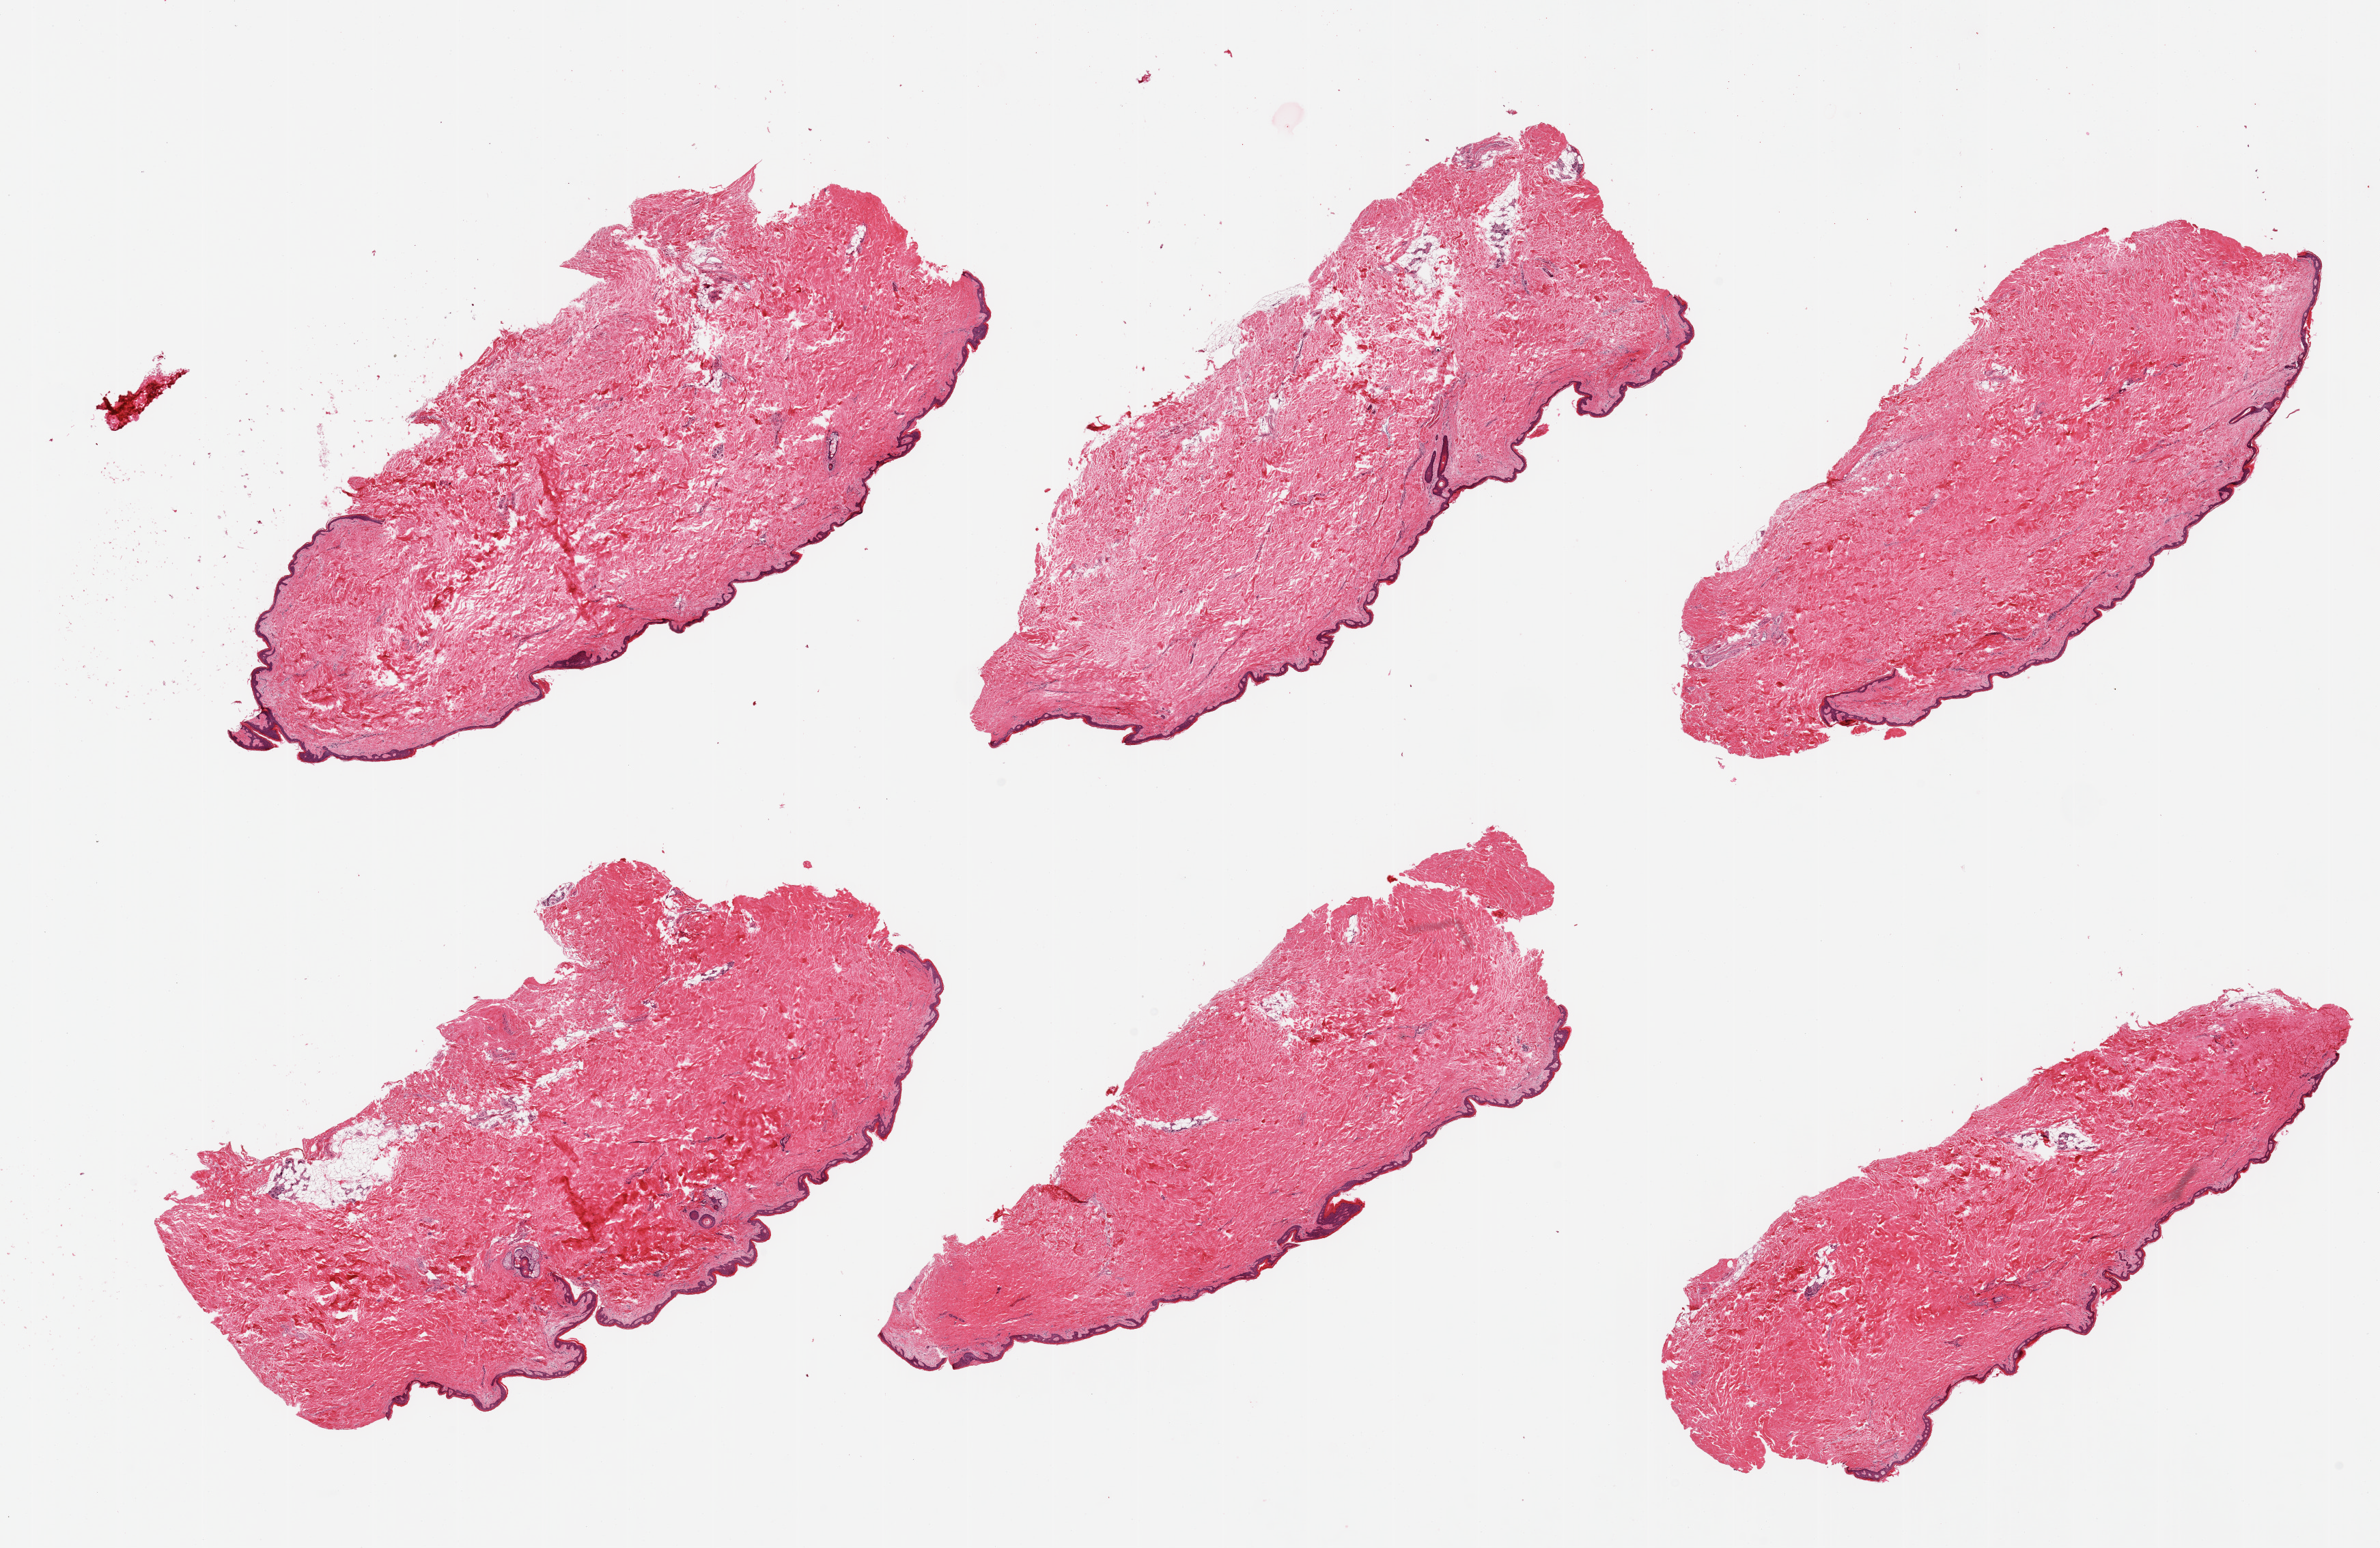
Digitized hematoxylin and eosin (H&E)-stained section, shown as a low-resolution overview of the whole scanned area (about 27.6 x 17.9 mm). PAXgene-fixed, paraffin-embedded tissue. Target tissue: skin of suprapubic region. Tissue donor sample. Donor sex: male.
Reviewer comment on this tissue sample: 6 pieces; ~10% internal fat.